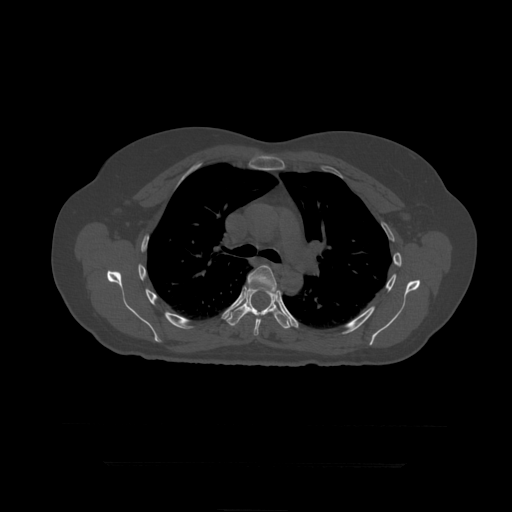
CT including the spine, one axial slice; slice 310 of 399 in the series (ordered by position); reconstruction kernel STANDARD; bone window (W 1800 / L 400 HU); 1.25 mm slice thickness; 512 × 512 image matrix, field of view 450 × 450 mm. Patient age 41 years. Case-level facts recorded for this patient, not image findings: primary cancer: breast.
Structures marked on this image (semi-automatically segmented with operator editing):
- T6 vertebra: bounding box (x1, y1, x2, y2) in pixels: (247, 265, 277, 336)
- T7 vertebra: (224, 286, 292, 329)